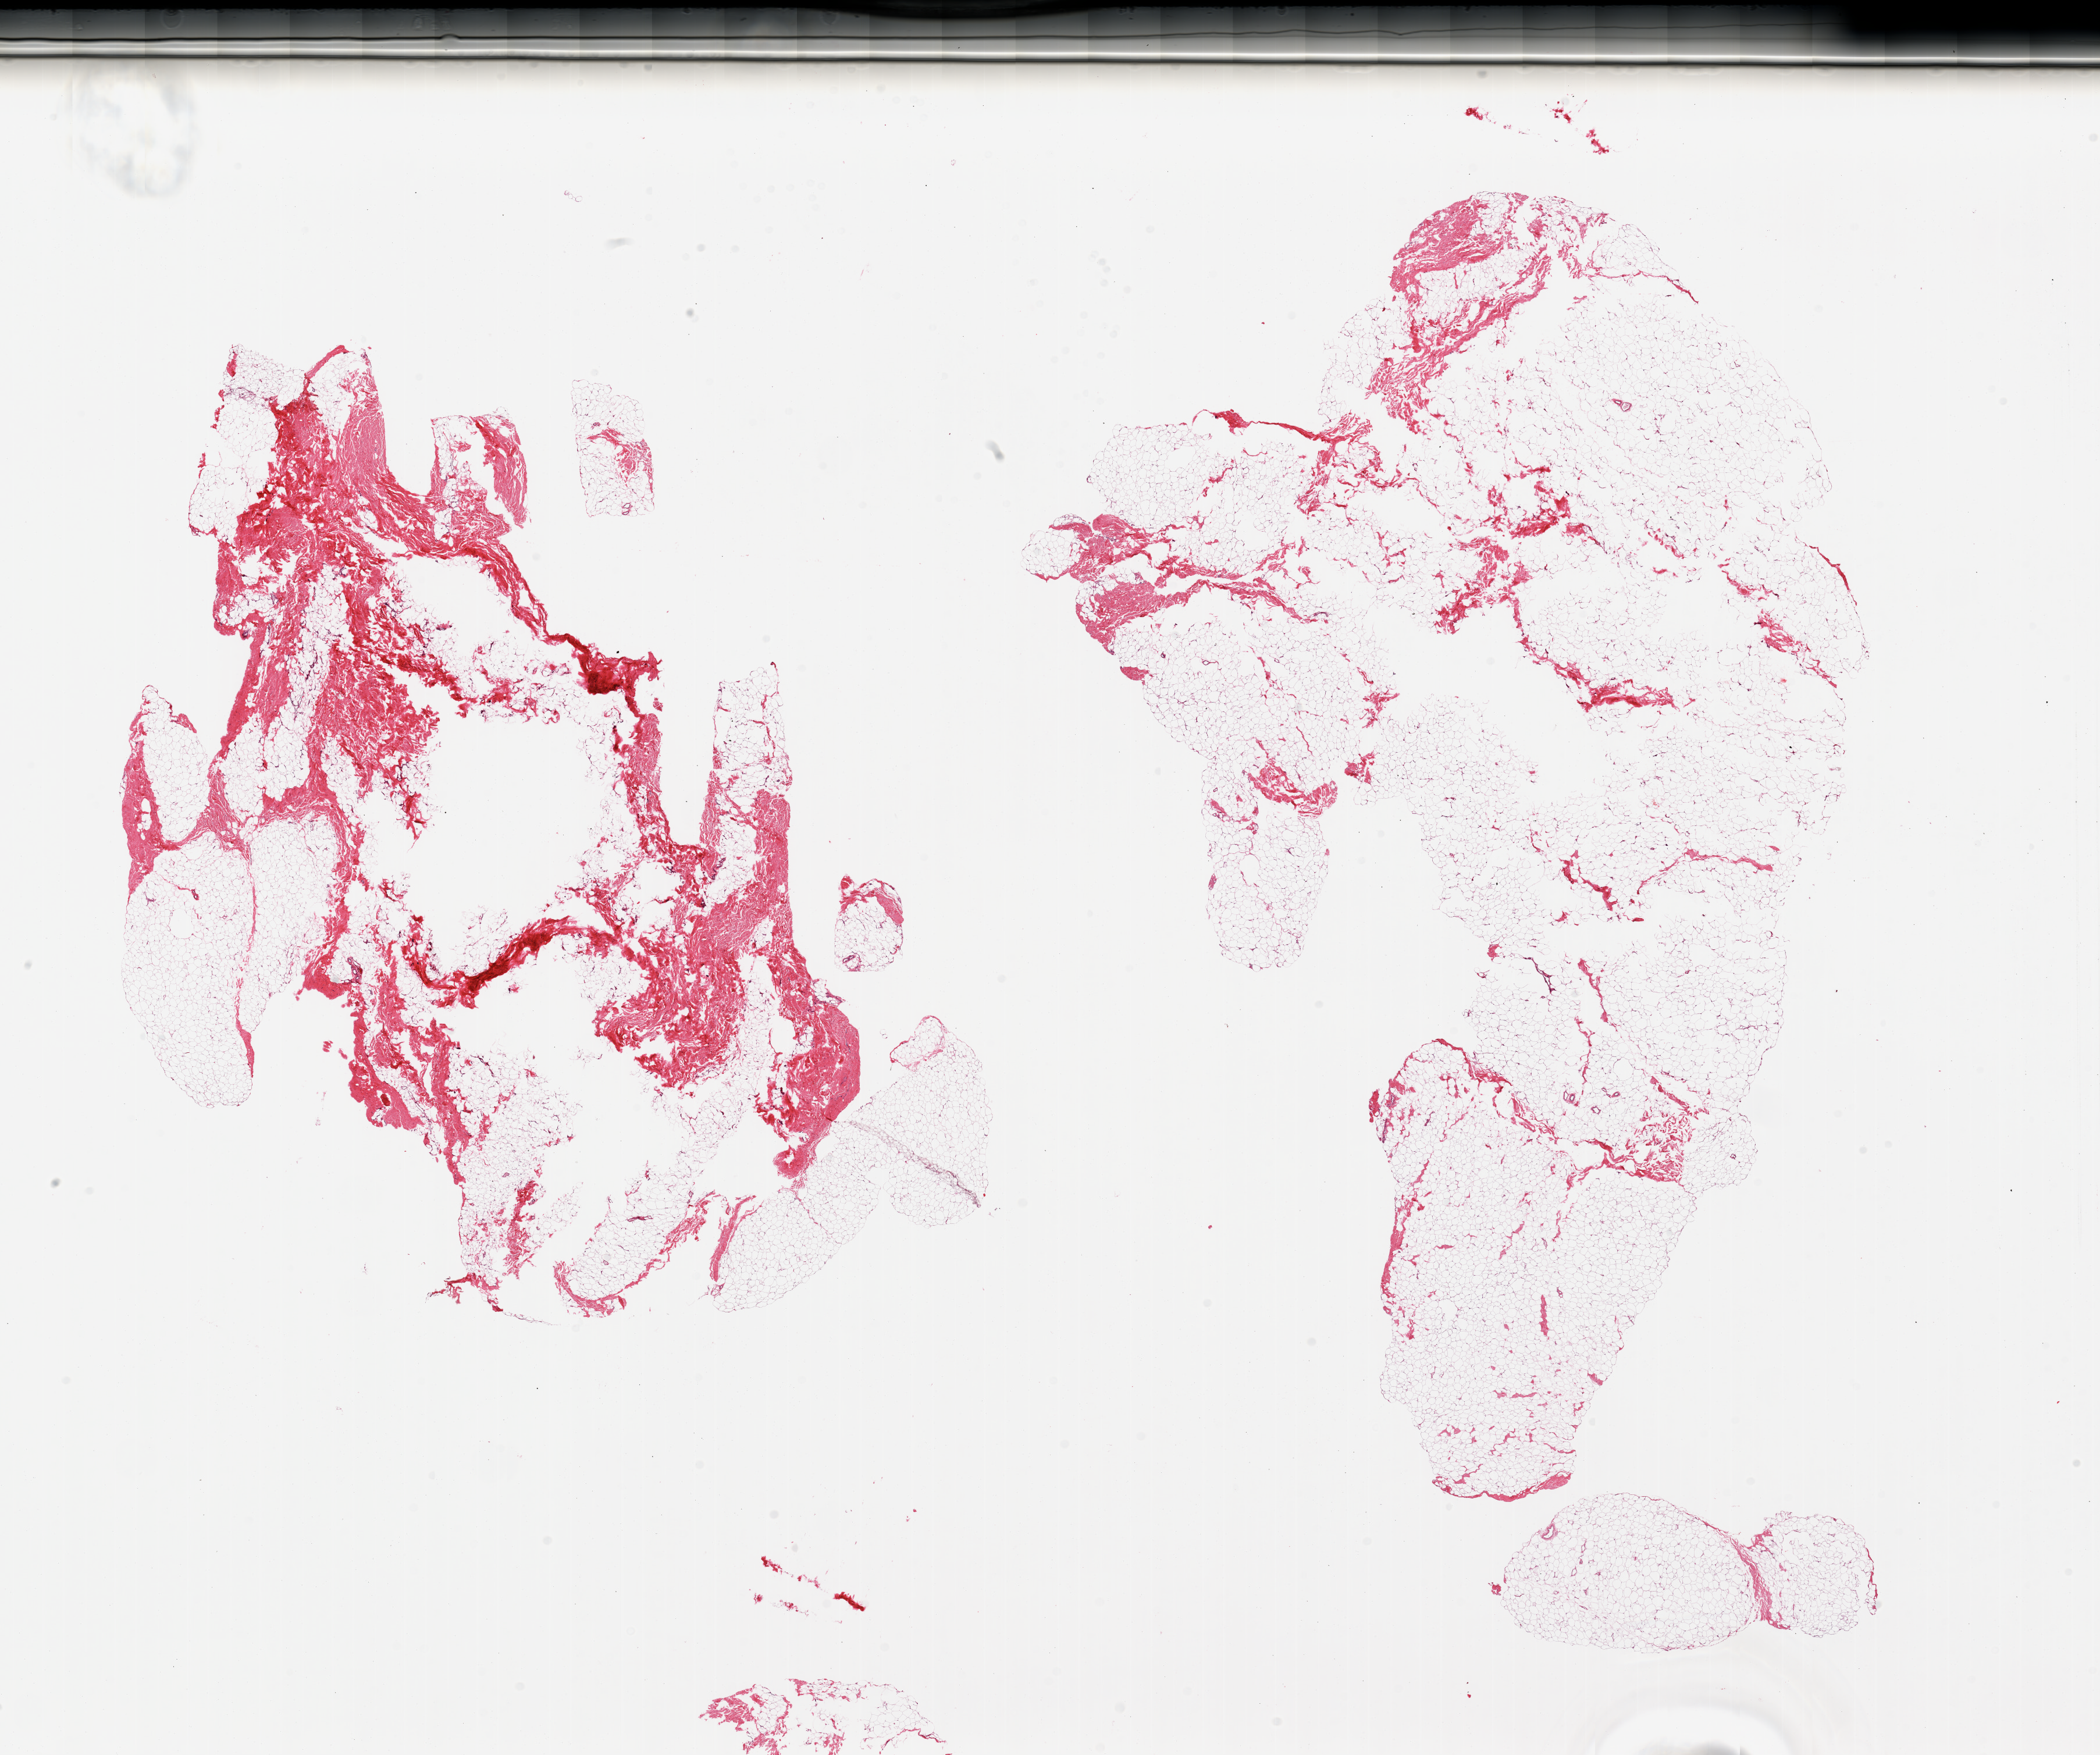
Whole-slide image, H&E stain — shown as a low-resolution overview of the whole scanned area (about 28.5 x 23.9 mm, acquisition: 20x scan); PAXgene-fixed, paraffin-embedded tissue; section of breast (target tissue); tissue donor sample. Donor sex: male.
Reviewer comment on this tissue sample: 2 pieces; fibrofatty tissue without mammary ductal elements.